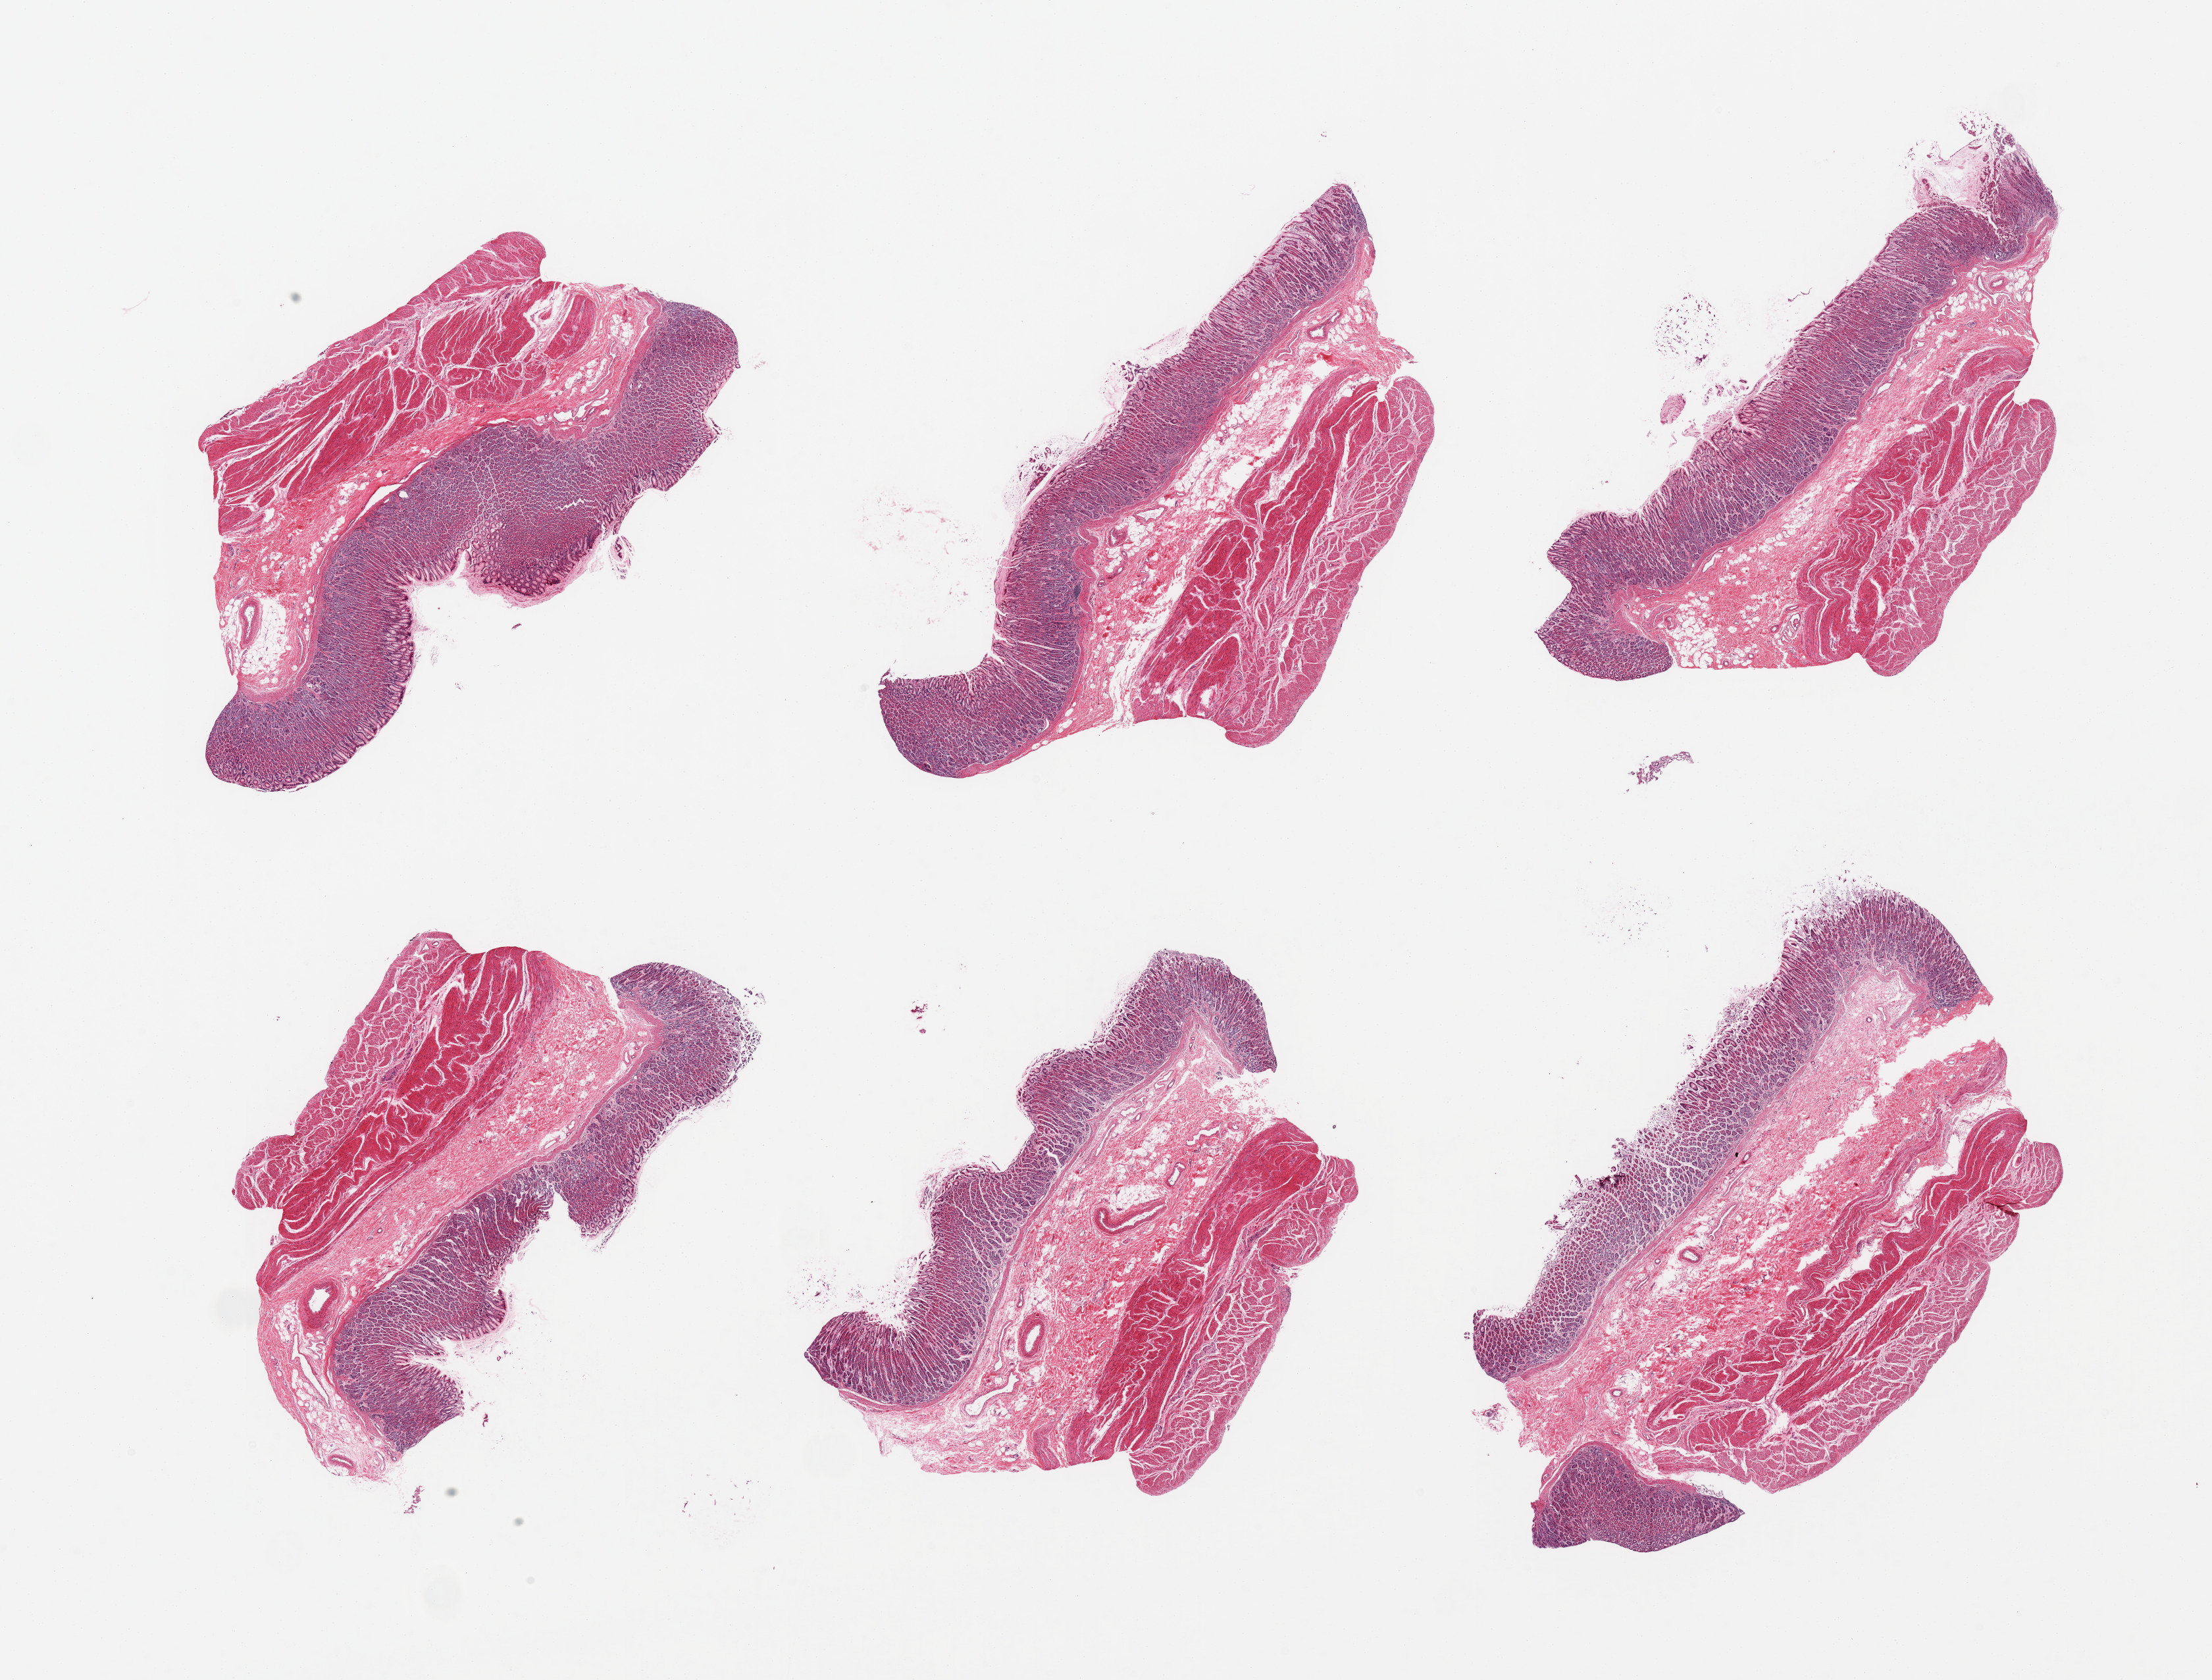
Digitized hematoxylin and eosin (H&E)-stained section — whole scanned area (about 26.6 x 20.2 mm, acquisition: 20x scan) shown as a low-resolution overview; PAXgene-fixed, paraffin-embedded tissue; target tissue: stomach; tissue donor sample. Donor sex: male.
Review note (as recorded): 6 pieces; full thickness sections, well preserved.